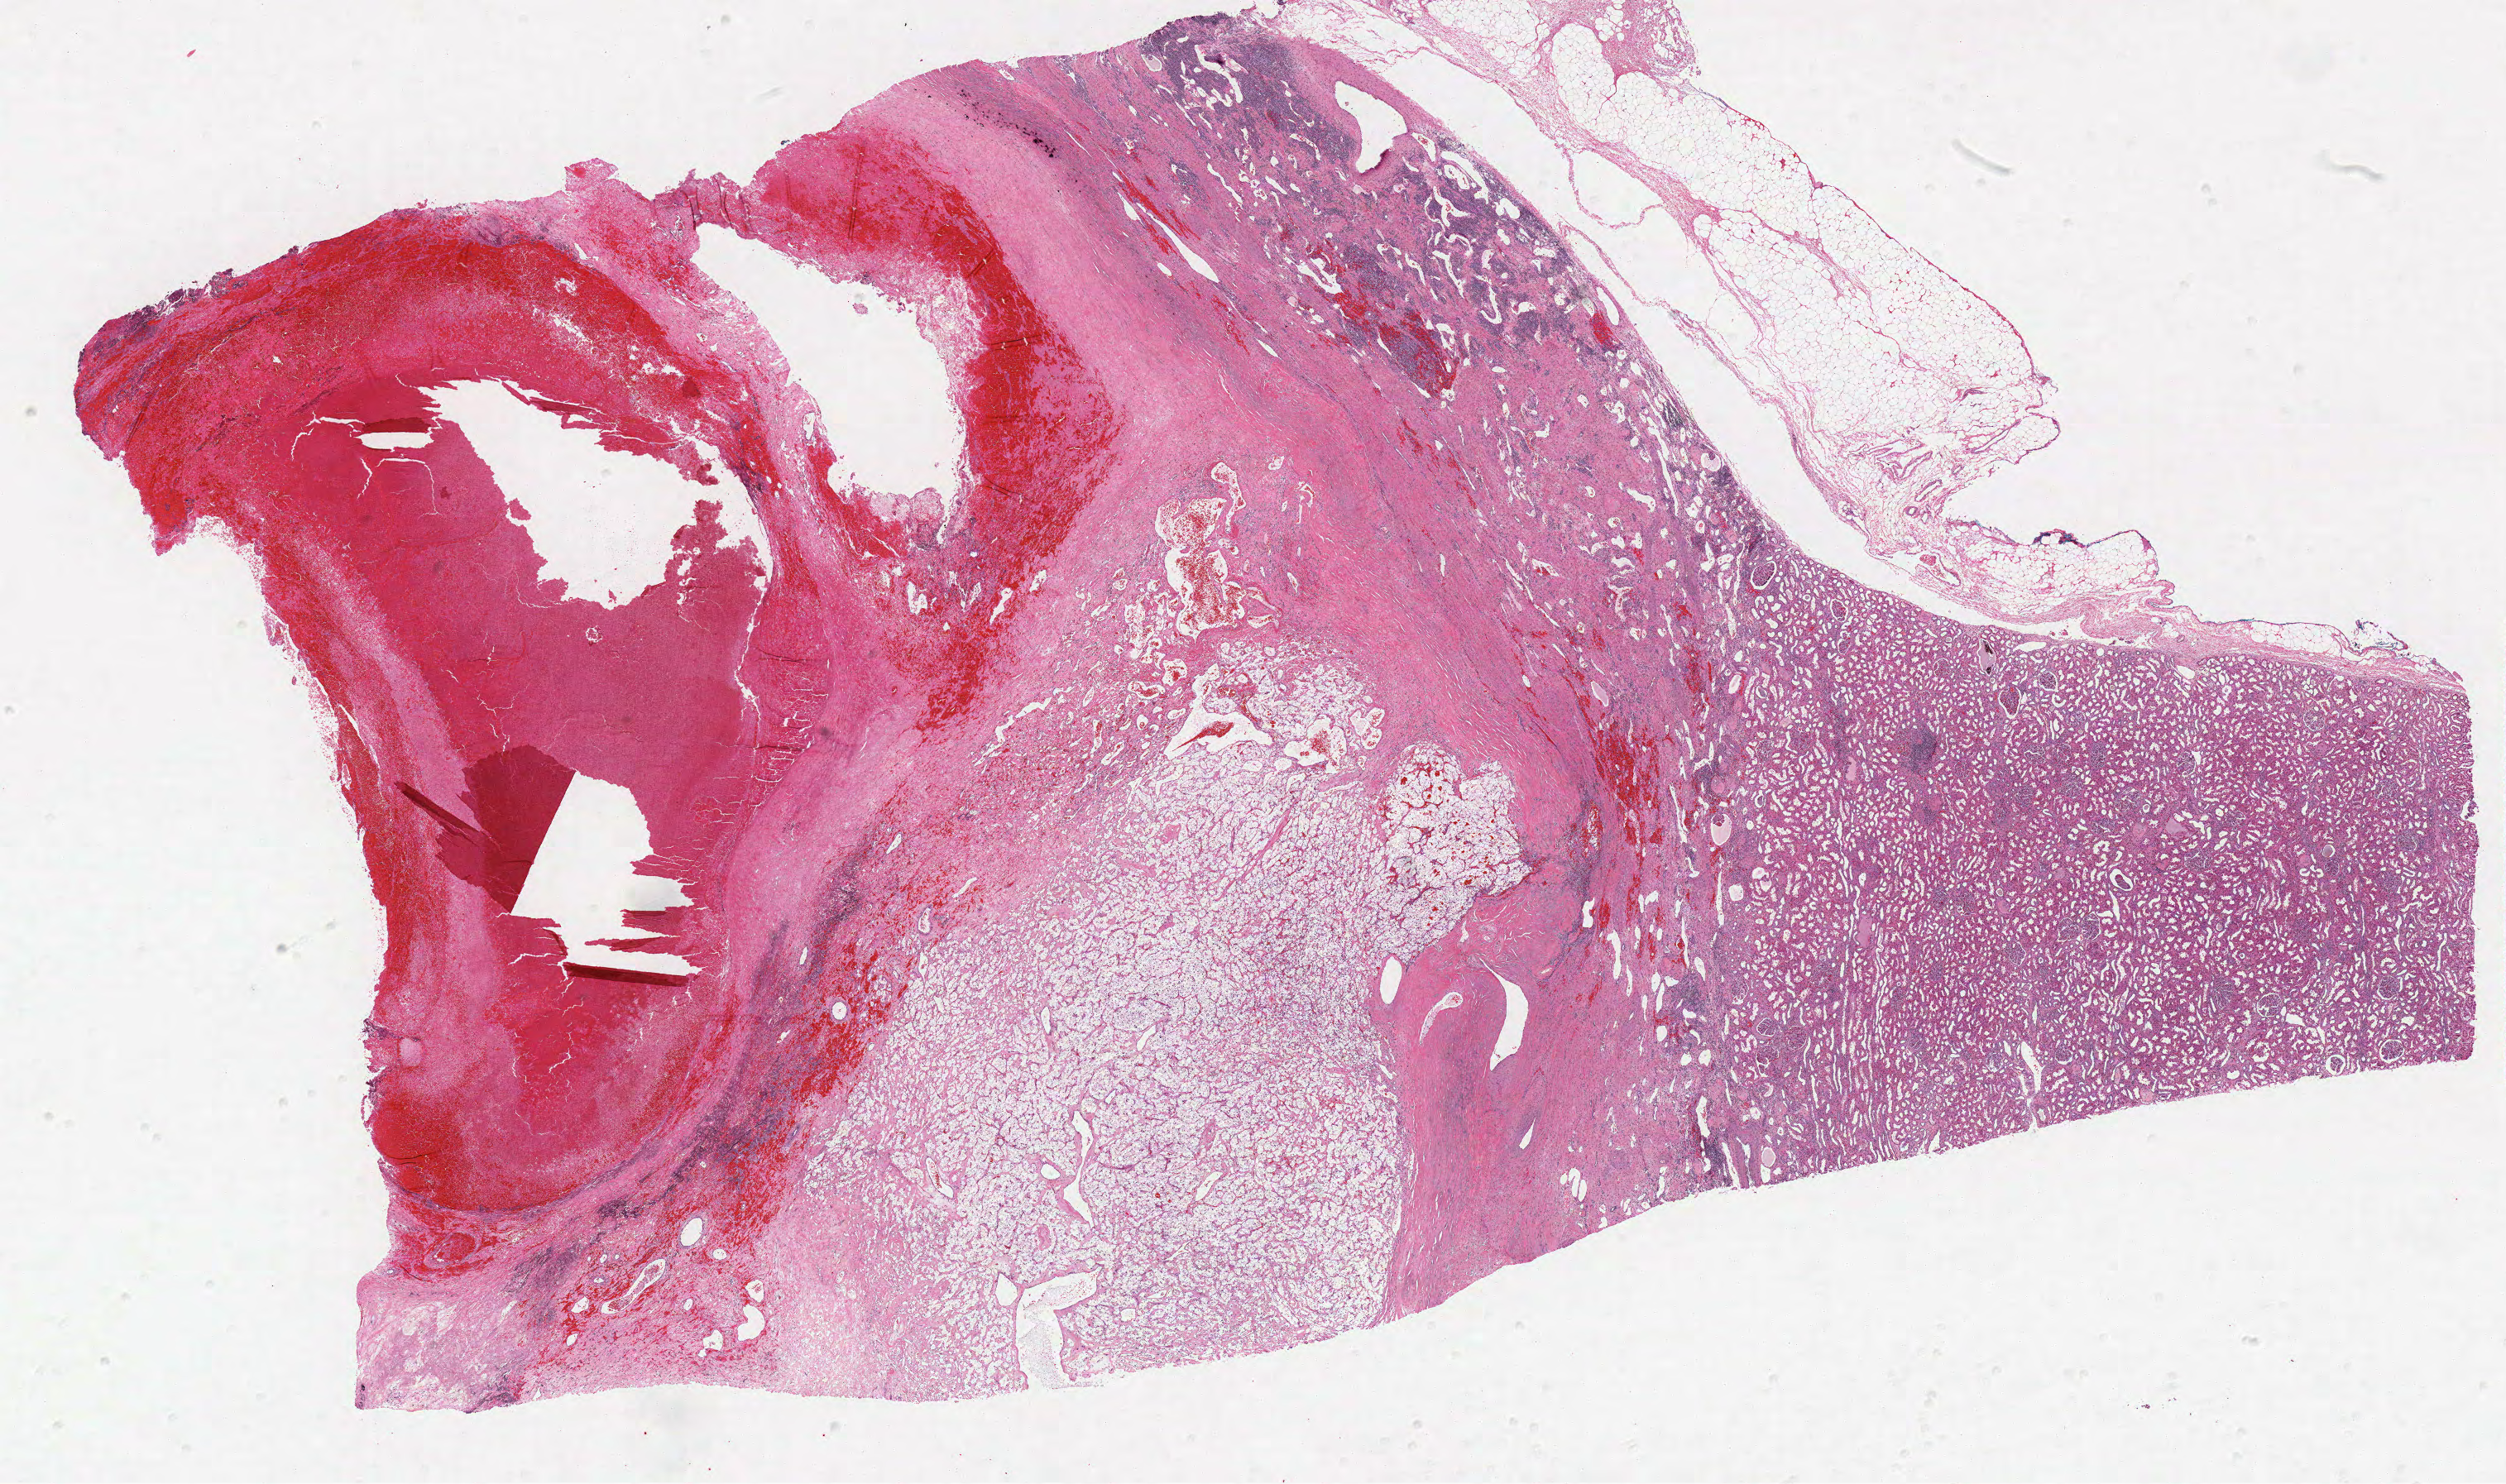
Digitized H&E tissue section (whole slide) — shown as a low-resolution overview of the whole scanned area (about 24.2 x 14.3 mm, slide scanned at 40x); formalin-fixed paraffin-embedded (FFPE) diagnostic section; sample: primary tumour, kidney. Male, age 59 years at initial diagnosis. Histologic grade: G2 (moderately differentiated).
AJCC pathologic stage: I. Diagnosis: Clear cell adenocarcinoma, NOS.